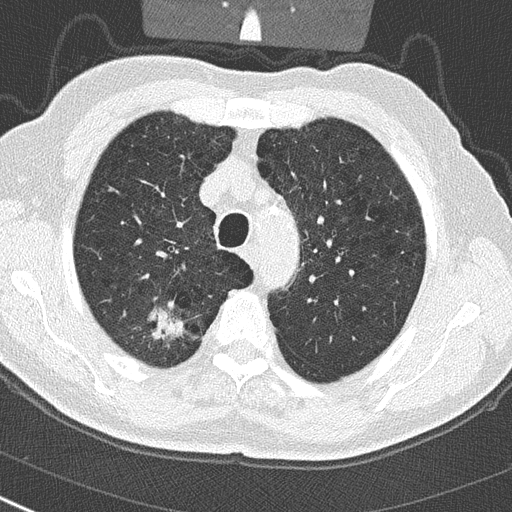
Low-dose screening chest CT, one axial slice. Position 223 of 290 along the scan axis. 120 kVp. Lung window (W 1500 / L -600 HU). 512 × 512 image matrix, field of view 300 × 300 mm.
Annotated regions visible in this slice (expert manual segmentation):
- lesion 1 (tumor, upper lobe of right lung): bounding box <143,309,187,350> (left, top, right, bottom; pixels)